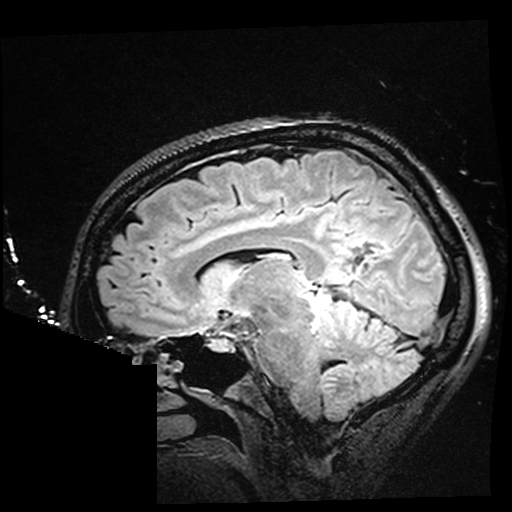
Brain MRI from a brain-tumour surgery series, one sagittal slice. Slice 99 of 176 in the series (ordered by position). T2 FLAIR. 1 mm slice thickness. 512 × 512 image matrix, field of view 250 × 250 mm. Case-level facts recorded for this patient, not image findings: histopathology: Oligodendroglioma; WHO grade: 2; IDH mutation: yes.
Structures marked on this image (manually delineated by an expert):
- residual tumour: bounding box <331,281,347,291> (left, top, right, bottom; pixels)